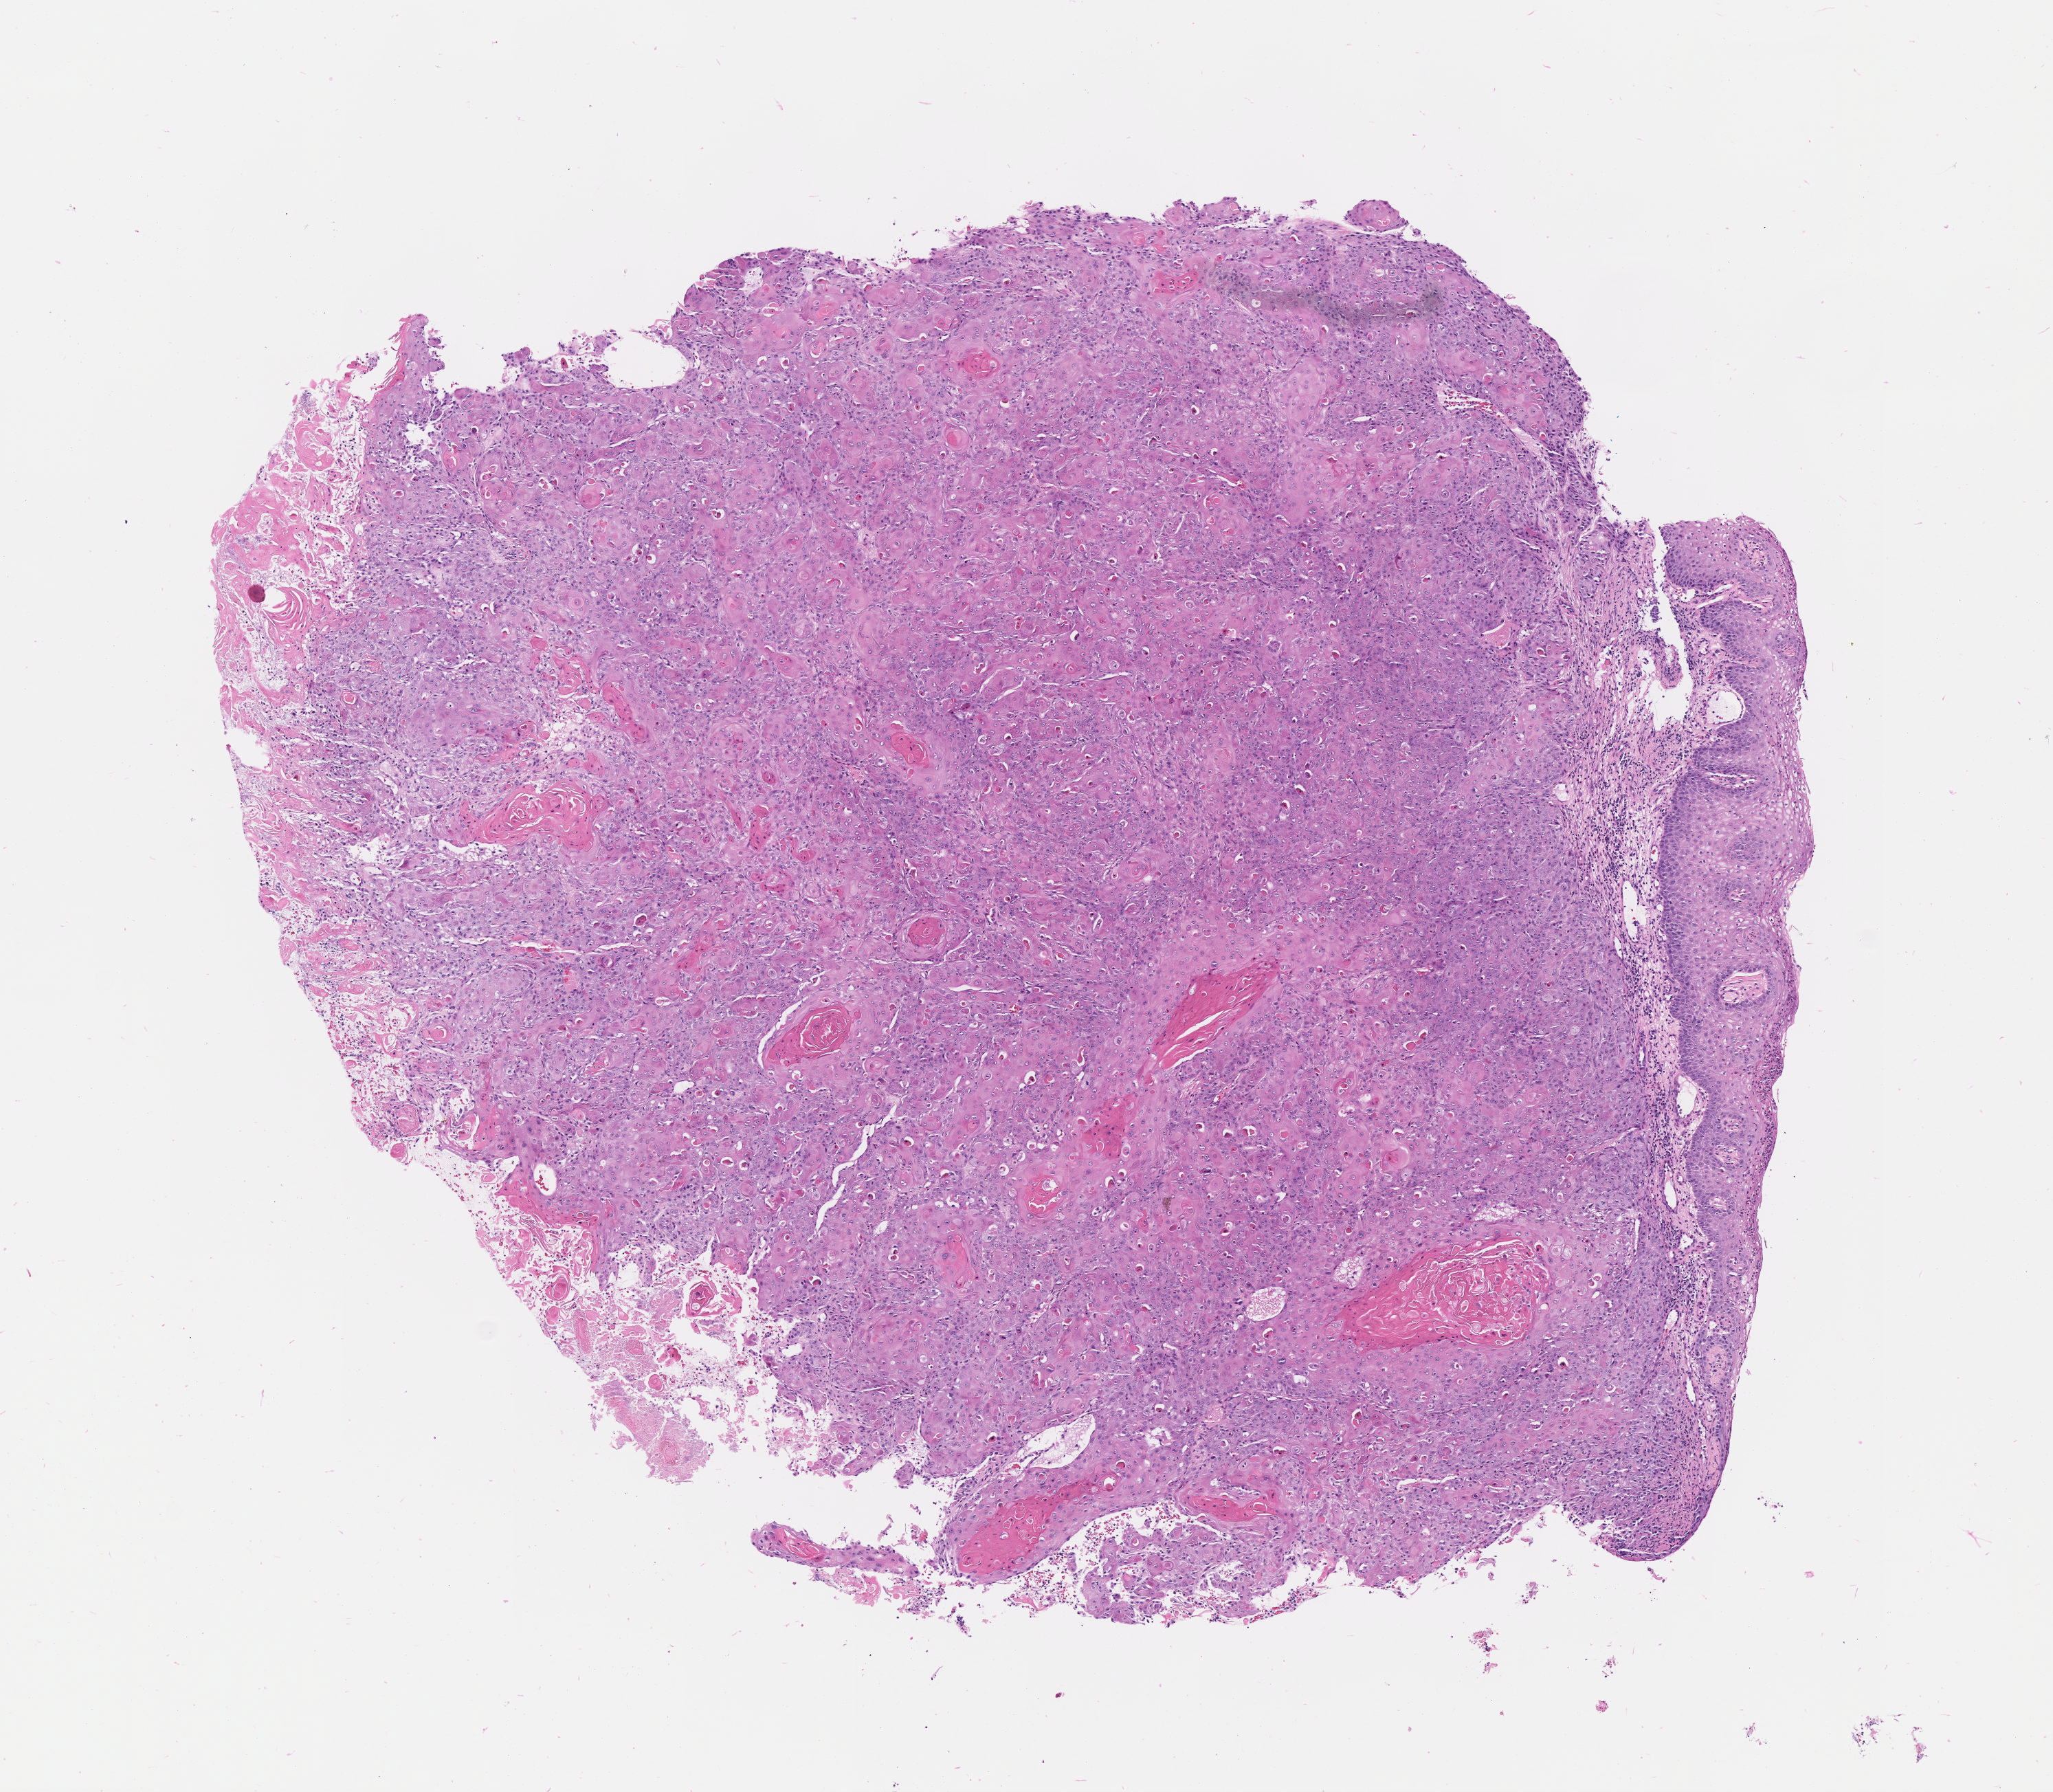
H&E whole-slide image — whole scanned area (about 6.0 x 5.3 mm) shown as a low-resolution overview. Specimen: tumor tissue. Anatomic site: cervix. Patient: female, aged 43.
Histologic diagnosis: Squamous cell carcinoma, keratinizing, NOS.